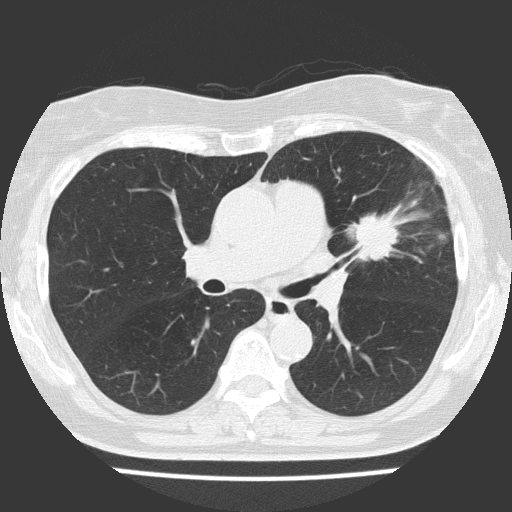
Low-dose screening chest CT, one axial slice. Position 87 of 151 along the scan axis. Reconstruction kernel FC51. 120 kVp. Lung window (W 1500 / L -600 HU). 2 mm slice thickness. 512 × 512 image matrix, field of view 309 × 309 mm.
Annotated regions visible in this slice (expert manual segmentation):
- lesion 1 (tumor, upper lobe of left lung): bounding box <356,213,400,261> (left, top, right, bottom; pixels)